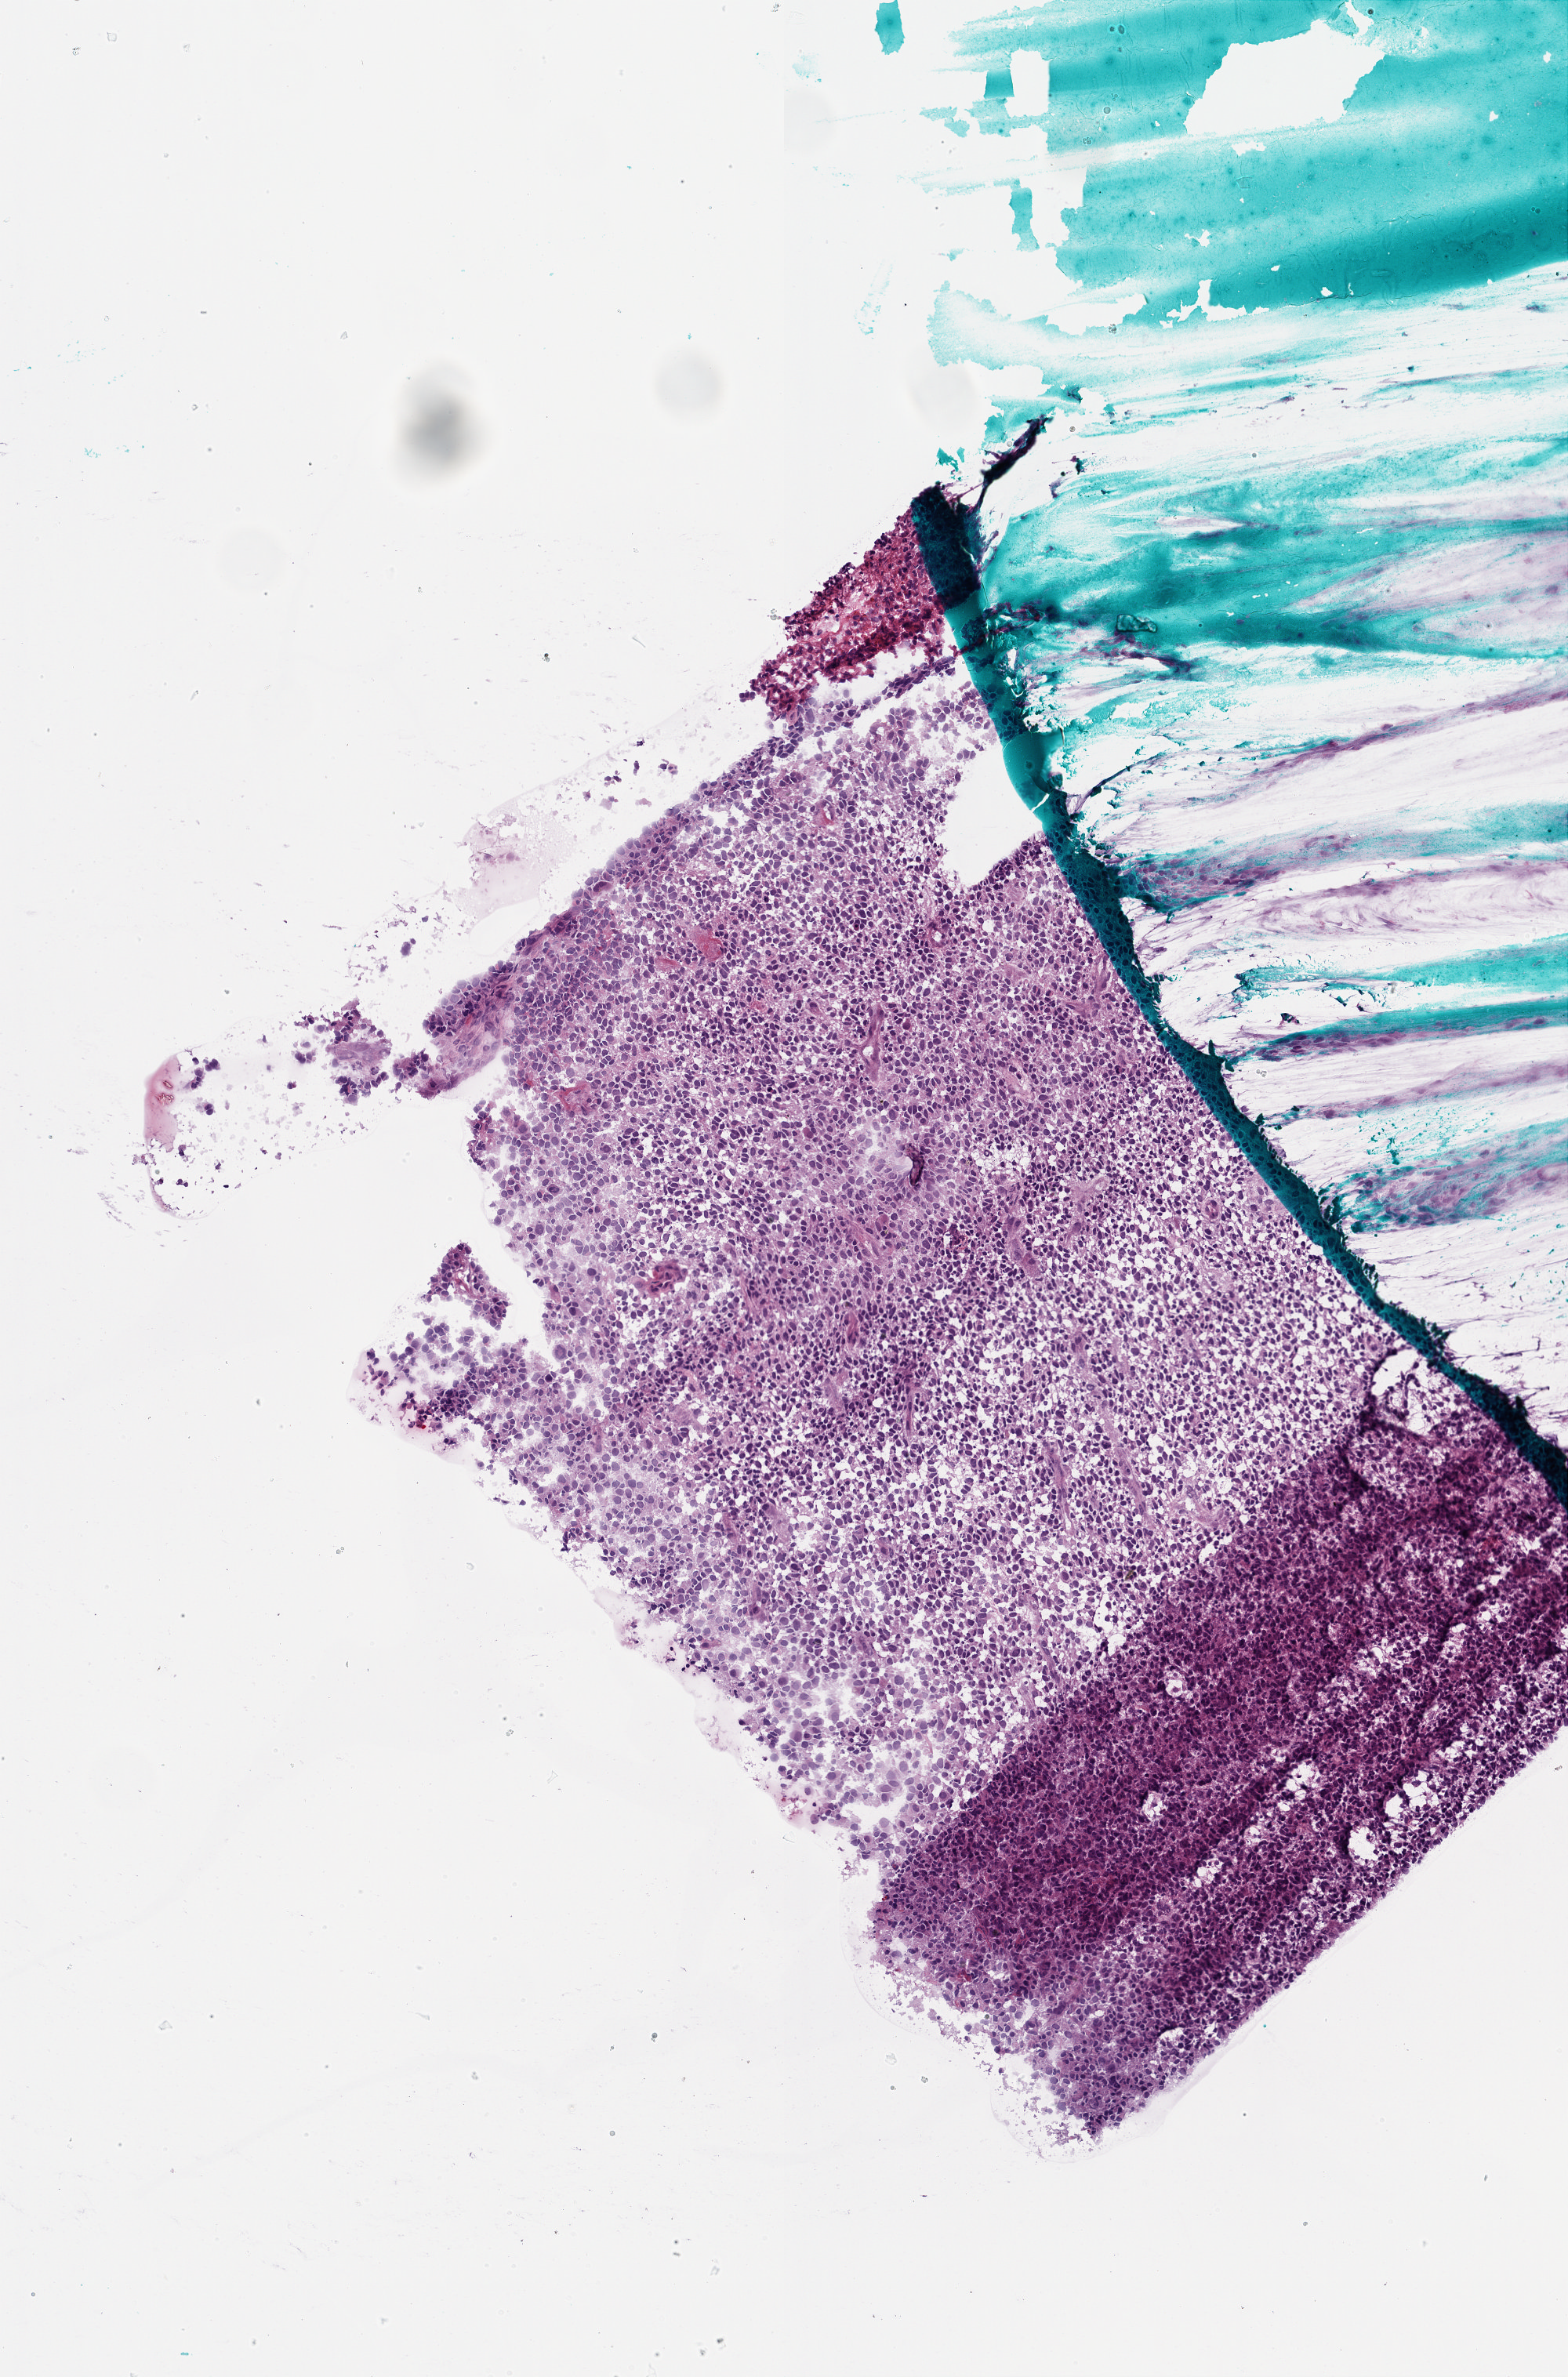
Hematoxylin and eosin (H&E) stained whole-slide image, whole scanned area (about 2.0 x 3.0 mm, from a 20x scan) shown as a low-resolution overview. Frozen section from the bottom of the tissue portion. Brain, primary tumour sample. Patient: male, age at initial diagnosis 51 years. Slide review estimates, as recorded: tumour cells 100%, tumour nuclei 100%, normal cells 0%, stromal cells 0%, necrosis 0%.
Diagnosis: Glioblastoma.